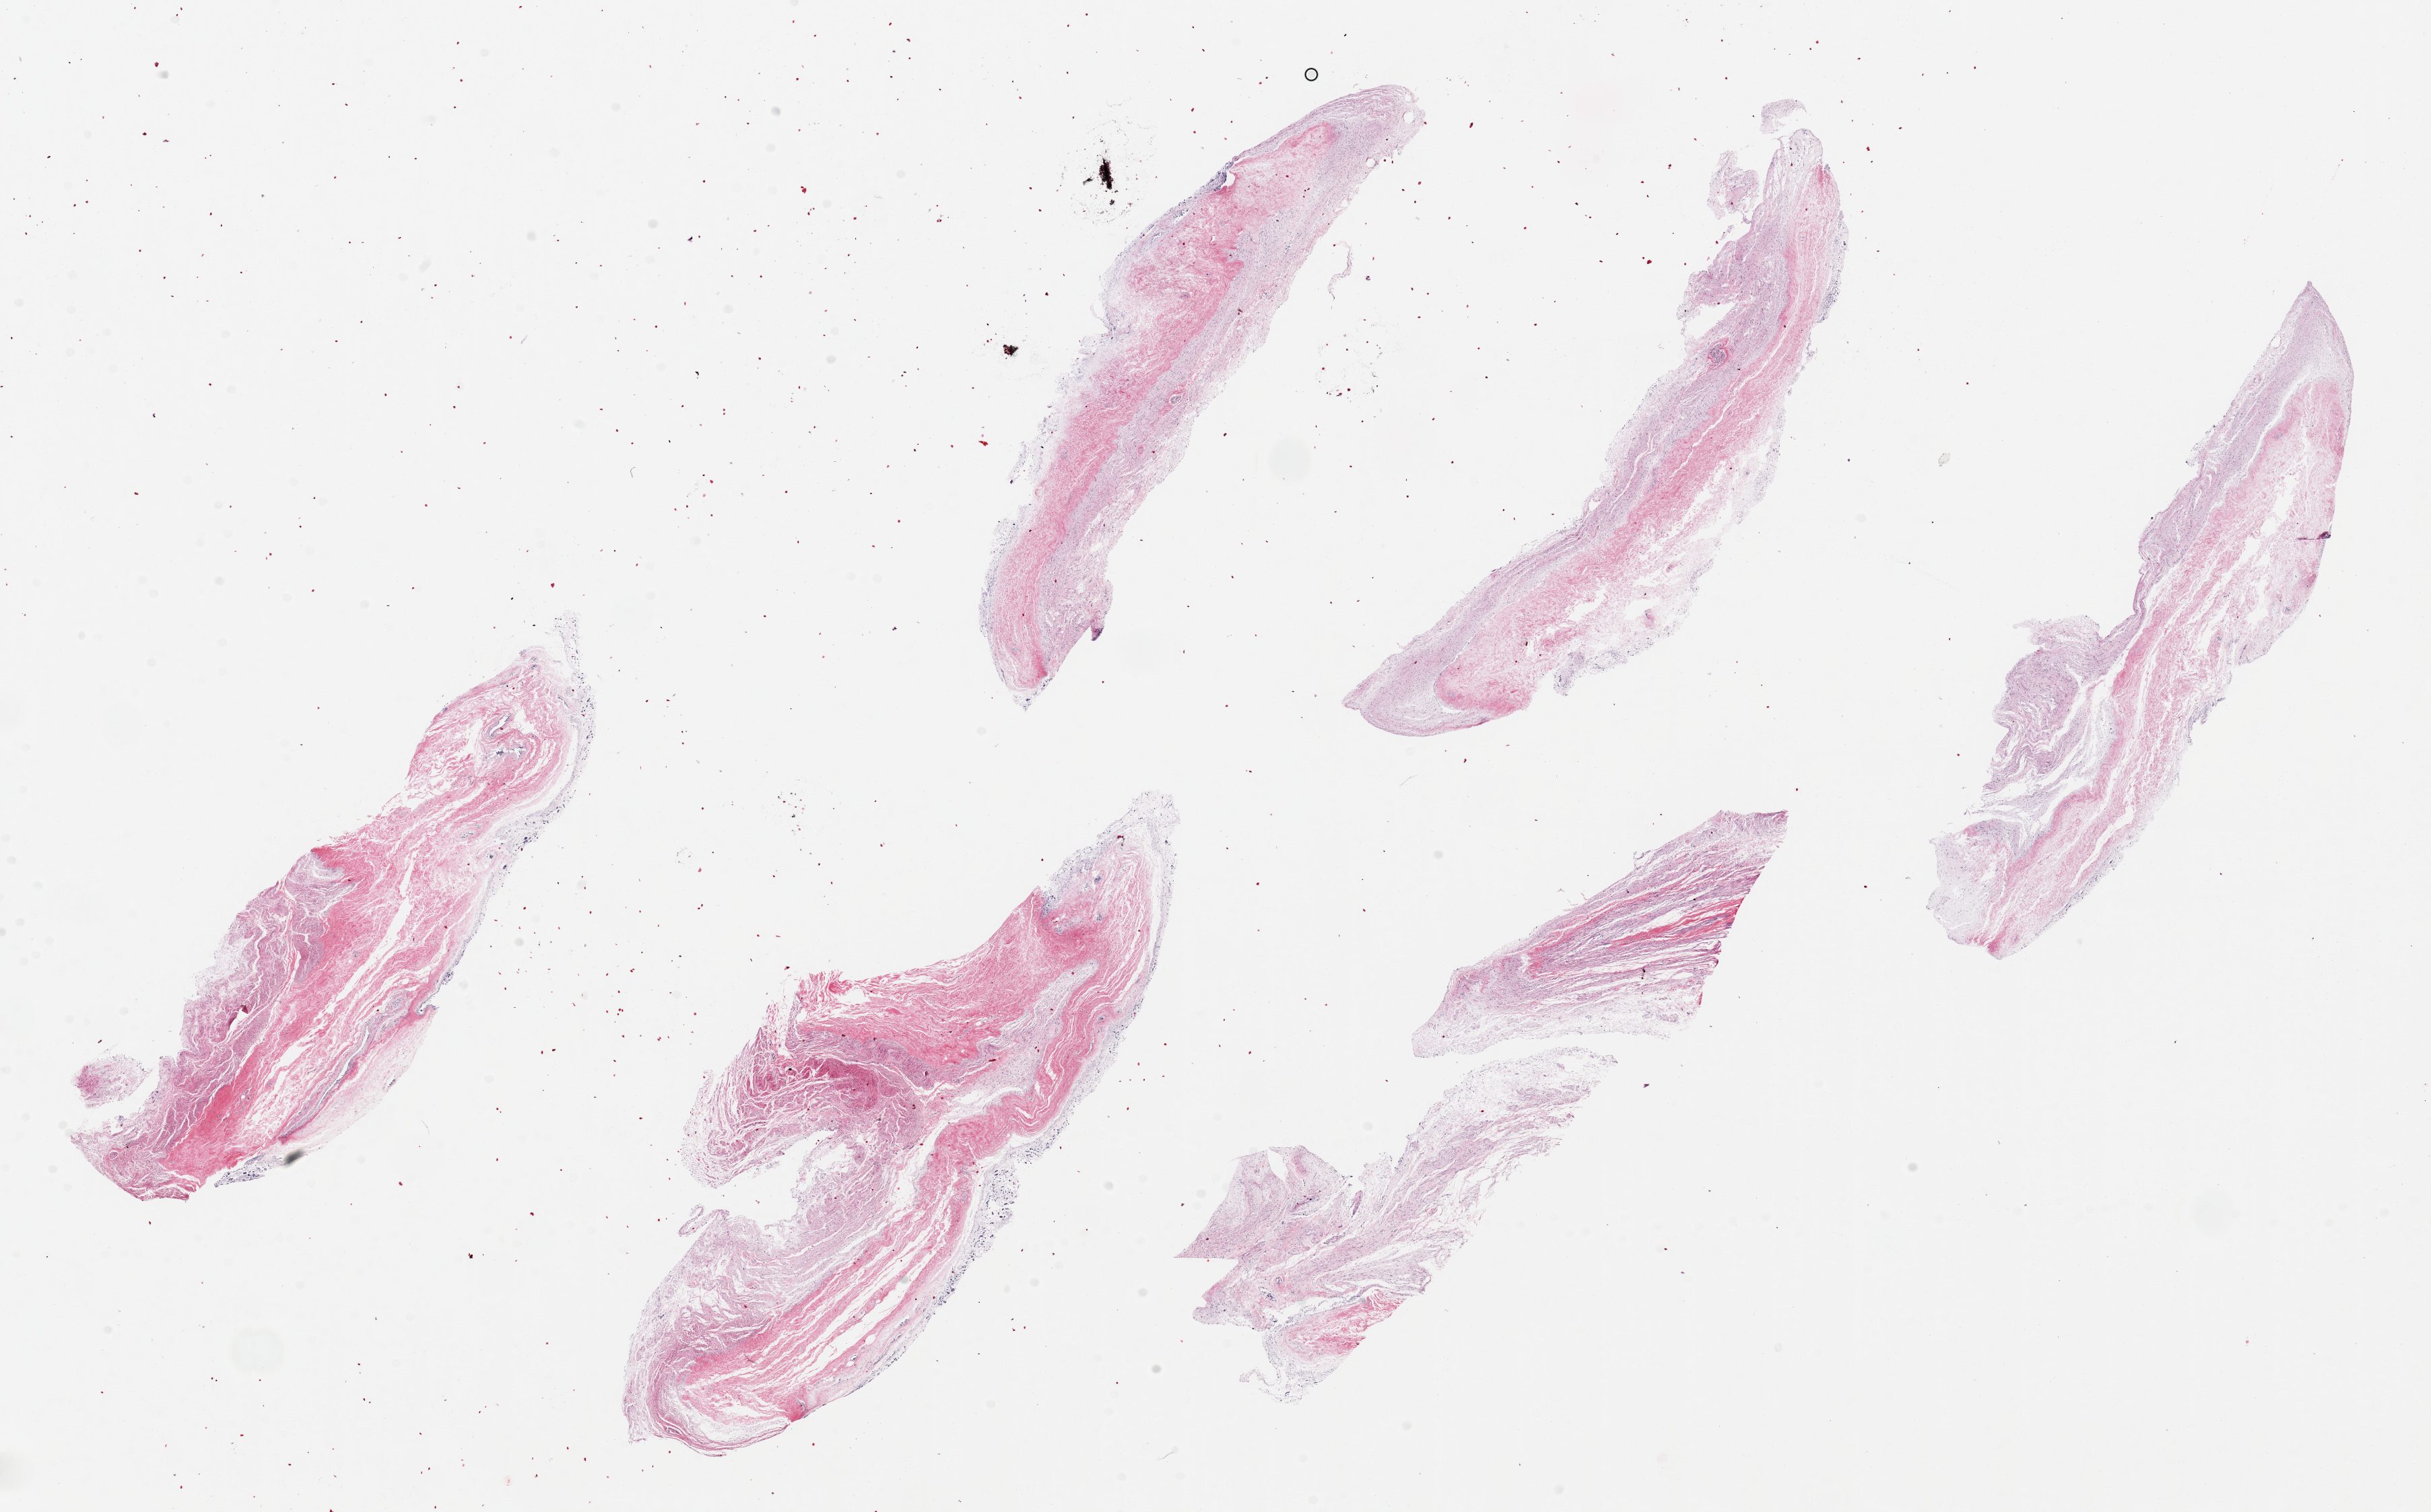
Whole-slide image, haematoxylin and eosin stain — shown as a low-resolution overview of the whole scanned area (about 28.5 x 17.8 mm, slide scanned at 20x). PAXgene-fixed paraffin-embedded (PFPE) section. Target tissue: stomach. Donor tissue sample. Donor sex: female.
Pathologist's review note for this sample: 6 pieces ~8x1.5mm, near total autolysis, mucosa sloughed.